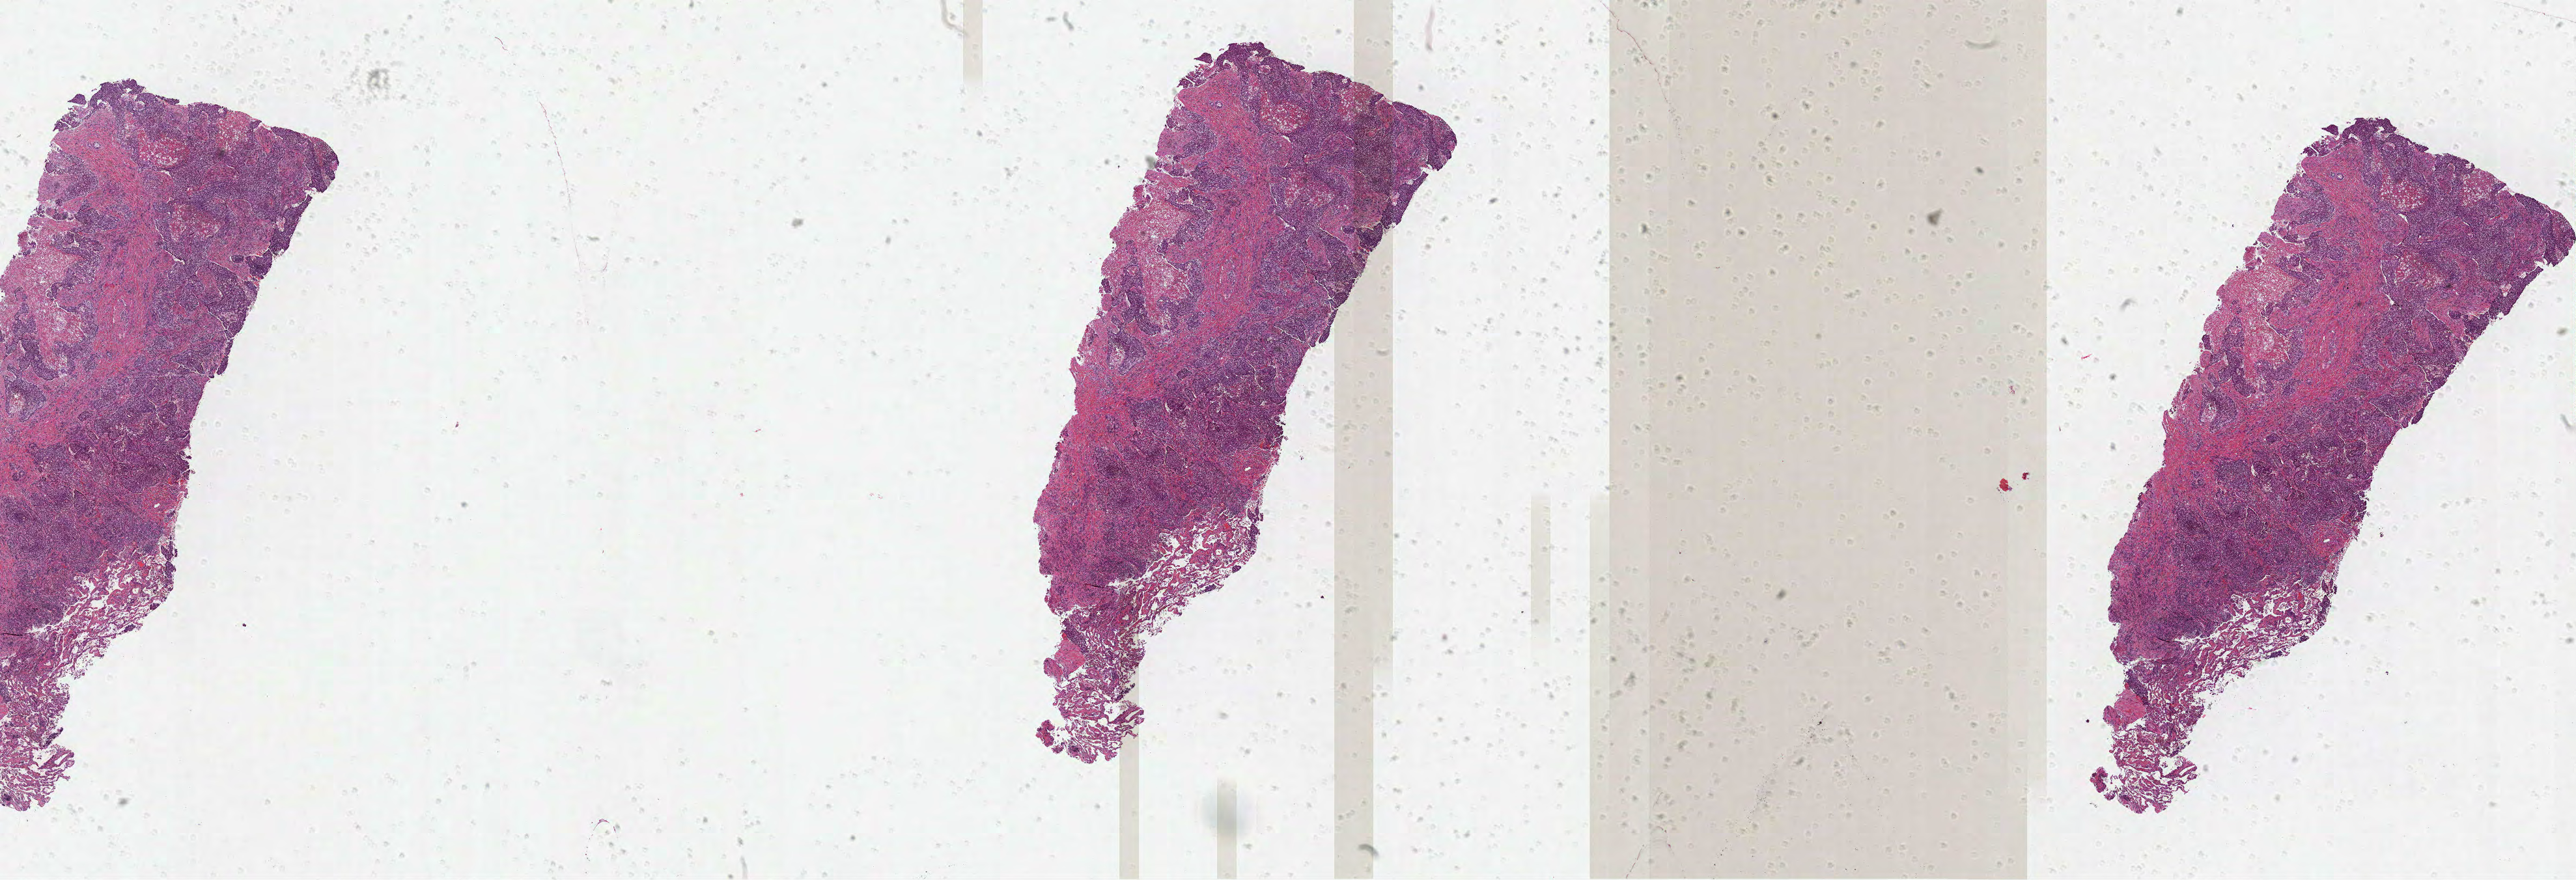
H&E whole-slide image — a low-resolution overview of the entire scanned area, about 31.9 x 10.9 mm (slide scanned at 40x), formalin-fixed paraffin-embedded (FFPE) diagnostic section, lung, primary tumour sample. Female, age 51 years at initial diagnosis.
Histologic diagnosis: Adenocarcinoma, NOS (lower lobe, lung).